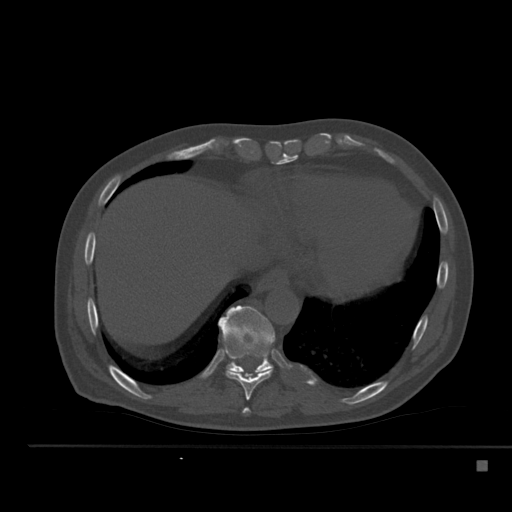
CT including the spine, one axial slice. Position 281 of 517 along the scan axis. 120 kVp. Bone window (W 1800 / L 400 HU). 1.5 mm slice thickness. 512 × 512 image matrix, field of view 408 × 408 mm. Male patient, age 70 years. From the clinical record (not read from this slice): primary cancer: renal; vertebrae with lytic lesions (as recorded): T4, T6, T10, T12, L3, L4, L5.
Outlined on this slice (semi-automatic segmentation, software-assisted and operator-edited):
- T10 vertebra: bounding box <218,305,275,376> (left, top, right, bottom; pixels)
- T8 vertebra: <242,408,250,414>
- T9 vertebra: <221,346,272,400>